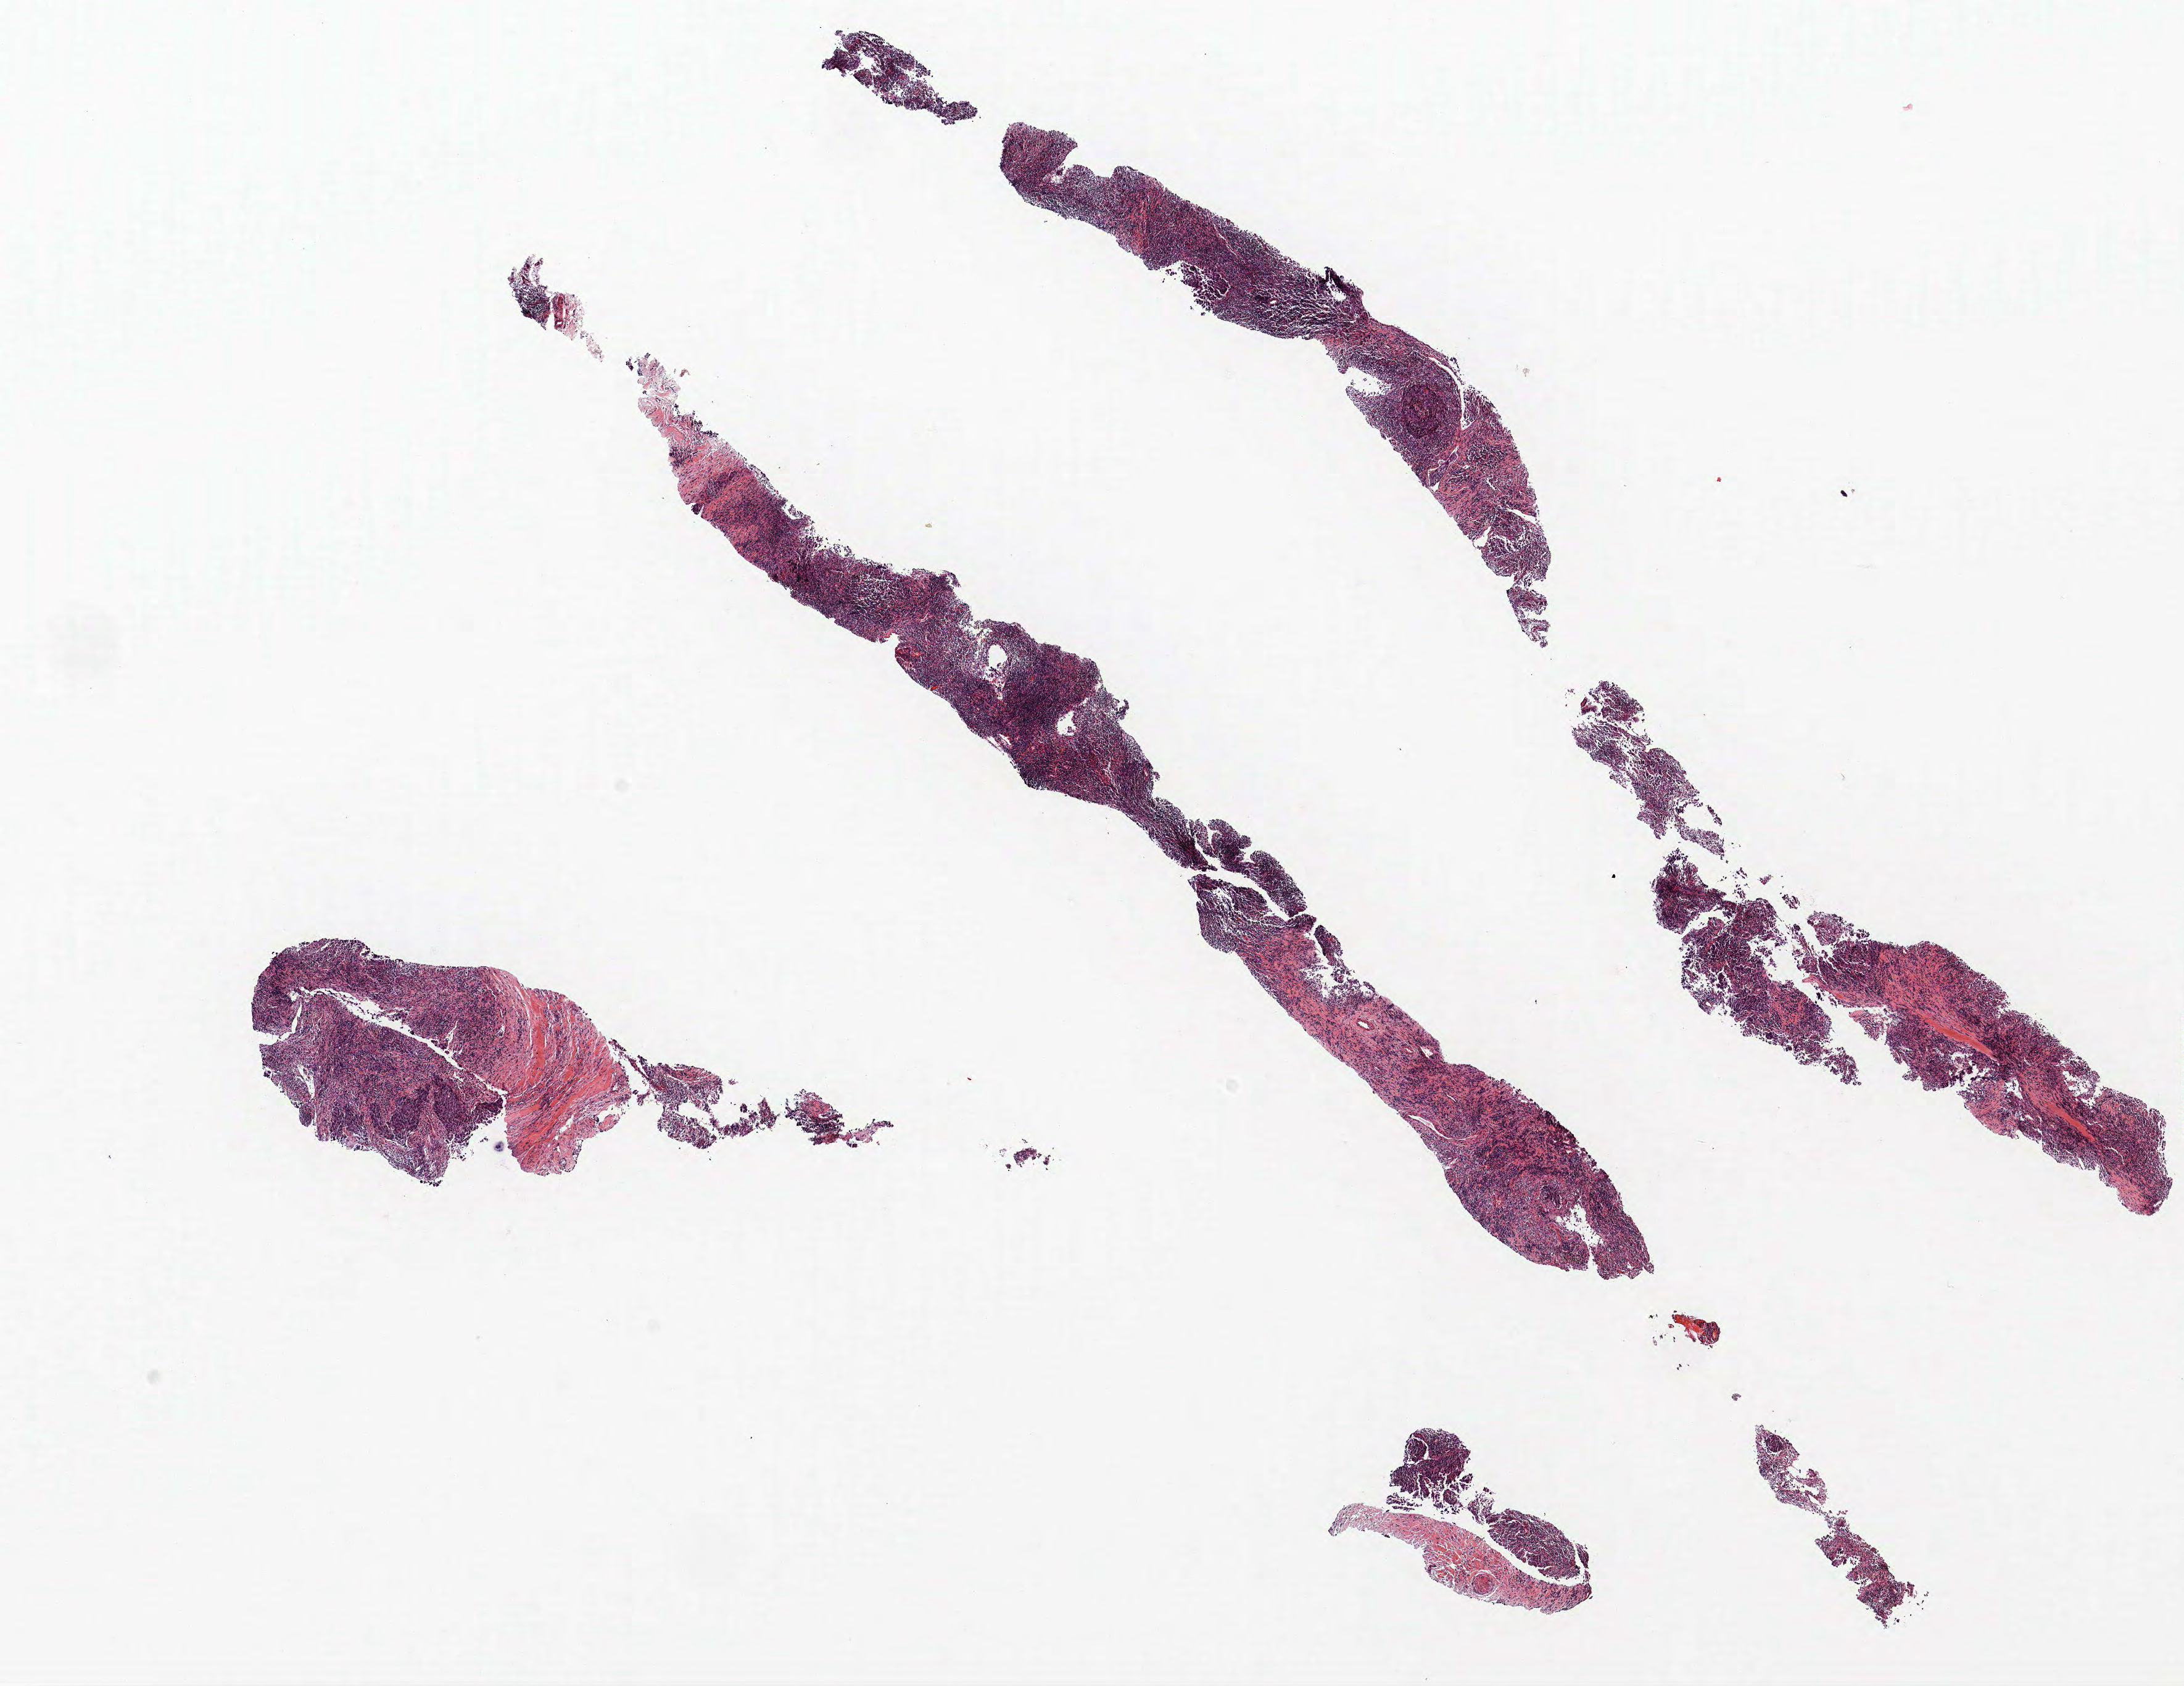
Hematoxylin and eosin (H&E) stained whole-slide image — a low-resolution overview of the entire scanned area, about 14.2 x 10.9 mm (slide scanned at 40x). Formalin-fixed paraffin-embedded (FFPE) section. Lung tissue. Male, age 69 at enrolment. Current smoker at enrolment. Grade: cannot be assessed (GX).
Participant's lung-cancer diagnosis: Carcinoma, NOS. Tumour size (pathology): 8 mm. Stage (AJCC 6th edition): IV. Primary tumour location (clinical record): right upper lobe.